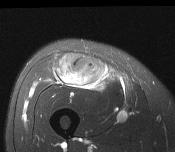
MRI of an extremity soft-tissue mass, one axial slice; position 69 of 116 along the scan axis; T2-weighted fat-saturated; MR volume resampled by the dataset authors to the PET/CT grid (not the native acquisition matrix); 3.27 mm slice thickness; 175 × 152 image matrix. Male patient. From the clinical record (not read from this slice): histological type: pleiomorphic leiomyosarcoma; grade: intermediate; site of the primary tumour: right thigh.
Outlined on this slice (expert contour drawn on MRI and transferred to this co-registered scan by the dataset authors):
- gross tumour volume including surrounding oedema: bounding box [x1, y1, x2, y2] px = [54, 54, 107, 89]
- gross tumour volume (mass): [70, 61, 102, 85]